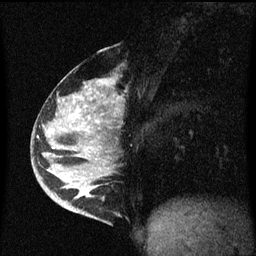
Breast MRI (dynamic contrast-enhanced), one sagittal slice; dynamic contrast-enhanced series, image 2 of 3 at this slice position (ordered by acquisition); 1.5 T; TE 4.2 ms, TR 8.4 ms; 2 mm slice thickness; 256 × 256 image matrix, field of view 200 × 200 mm. Female patient, age 34 years. From the clinical record (not read from this slice): setting: breast cancer imaged before/during neoadjuvant chemotherapy; receptor status: HR-positive, HER2-negative.
Annotated regions visible in this slice (semi-automatic segmentation, software-assisted and operator-edited):
- analysis volume of interest (the breast-tissue region the enhancement analysis was run in; not a lesion): bounding box (x1, y1, x2, y2) in pixels: (34, 48, 119, 215)
- tumour enhancement mask (voxels above the 70 % enhancement threshold inside the analysis volume of interest): (66, 82, 101, 197)